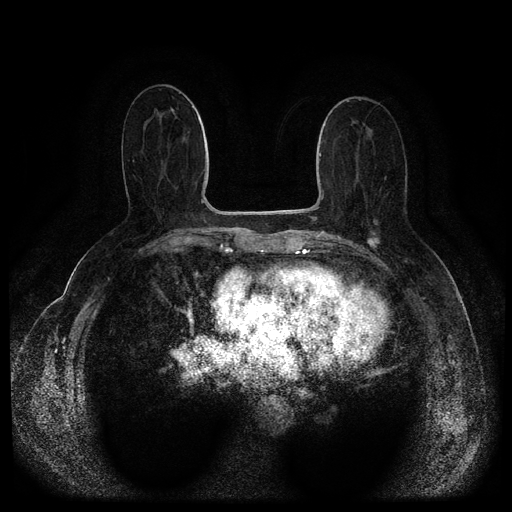
Breast MRI (dynamic contrast-enhanced, multi-phase), one axial slice. Position 44 of 116 along the scan axis. Dynamic contrast-enhanced series, time point 2 of 5 at this slice position (early post-contrast). 1.5 T. TE 2.6 ms, TR 5.4 ms. 2 mm slice thickness. 512 × 512 image matrix. Patient: female, 67 years.
Structures marked on this image (semi-automatically segmented with operator editing):
- breast lesion (labelled 'tumour' in the annotation; benign lesions carry a separate 'benign' label): bounding box [x1, y1, x2, y2] px = [367, 233, 382, 250]